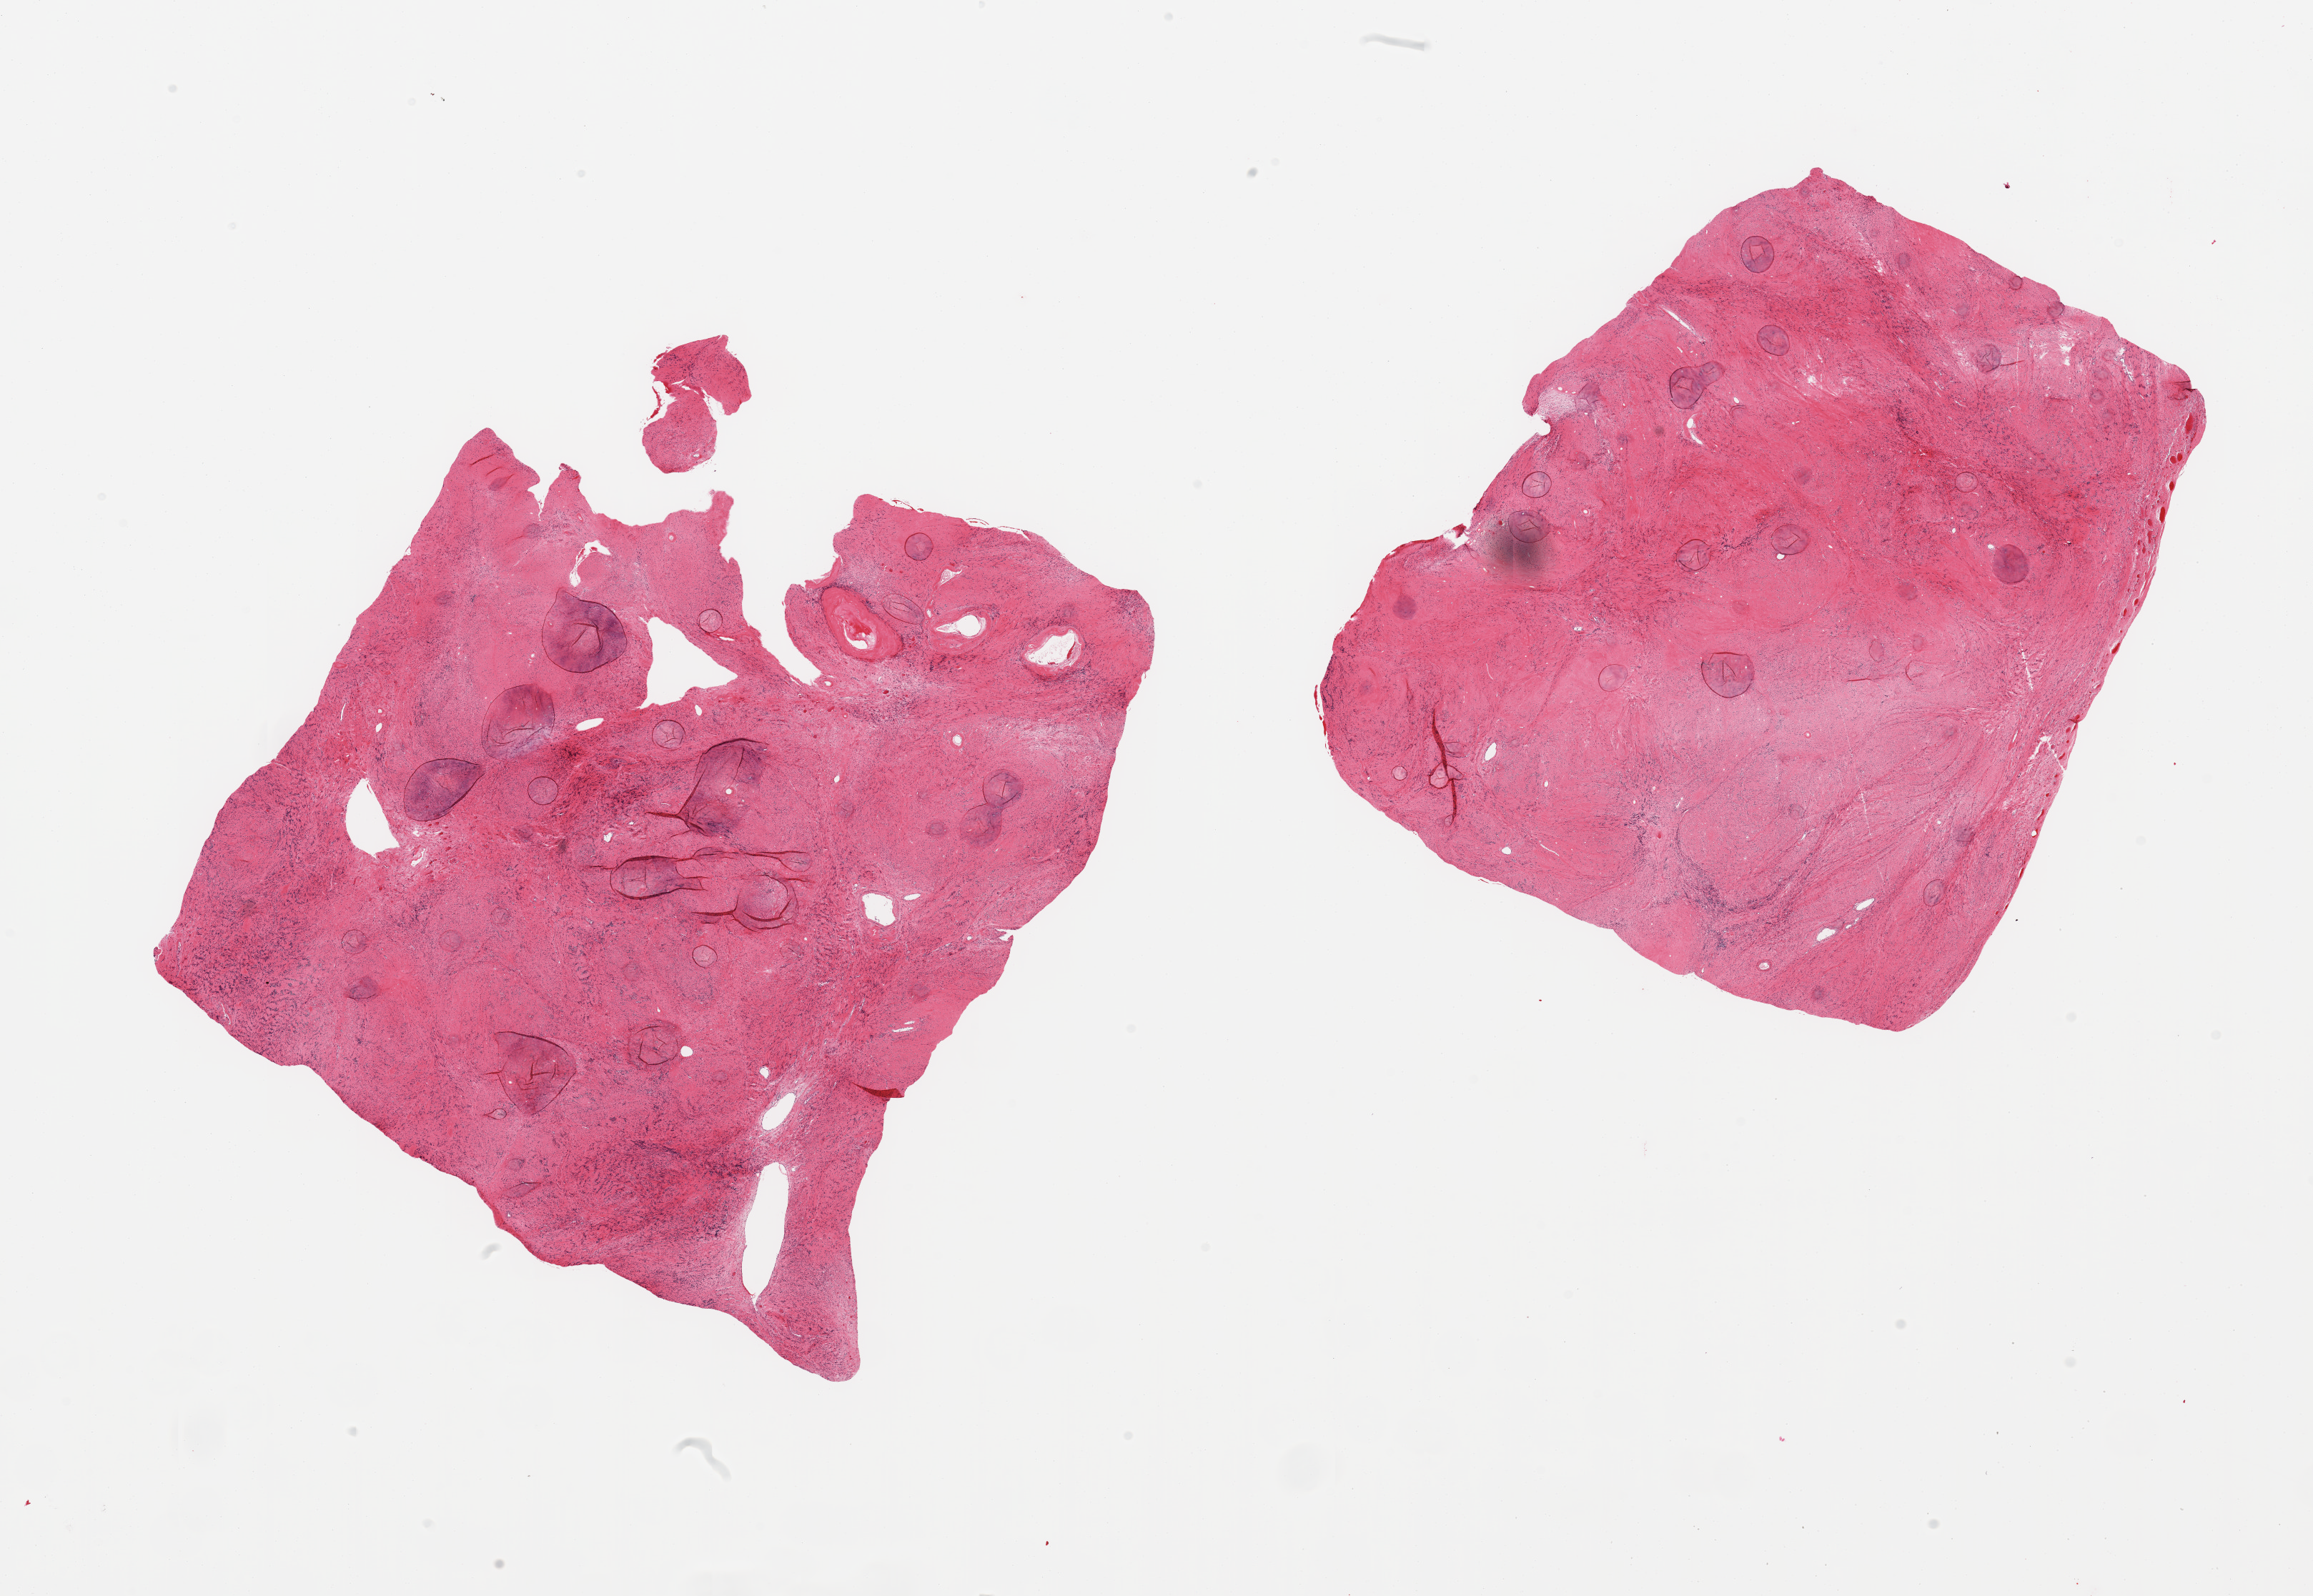
Whole-slide image, hematoxylin and eosin (H&E) stain, low-resolution overview of the scanned area, about 25.6 x 17.7 mm (from a 20x scan). PAXgene-fixed, paraffin-embedded tissue. Section of uterus (target tissue). Donor tissue sample.
Reviewer comment on this tissue sample: 2 pieces, unusually advanced autolysis.